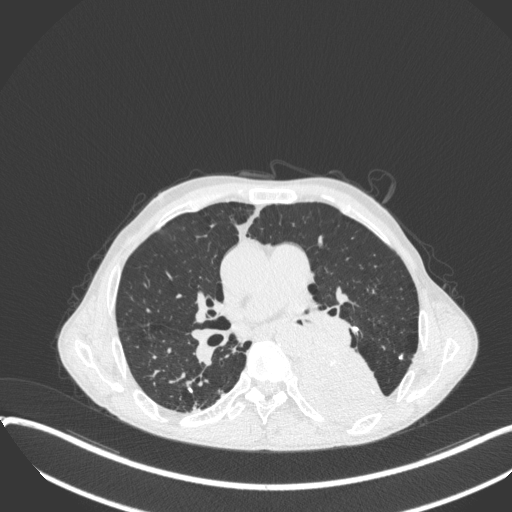
Chest CT, one axial slice; position 208 of 400 along the scan axis; reconstruction kernel B31f; 120 kVp; lung window (W 1500 / L -600 HU); 1 mm slice thickness; 512 × 512 image matrix. Patient: male, 57 years. Case-level facts recorded for this patient, not image findings: clinical TNM (as recorded): T4 N0 M0.
Structures marked on this image (rectangle marked by the reading radiologist):
- lung tumour (recorded histology: squamous cell carcinoma): bounding box <291,346,387,422> (left, top, right, bottom; pixels)